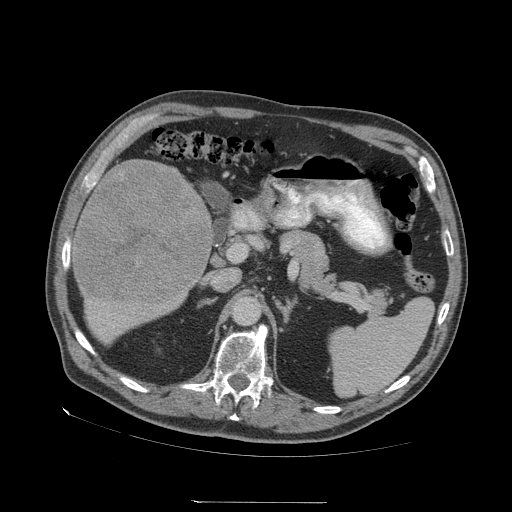
Contrast-enhanced abdominal CT (liver protocol), one axial slice. Slice 25 of 83 in the series (ordered by position). Reconstruction kernel STANDARD. 140 kVp. Soft-tissue window (W 400 / L 40 HU). 512 × 512 image matrix, field of view 460 × 460 mm. From the clinical record (not read from this slice): diagnosis: hepatocellular carcinoma (patient treated with transarterial chemoembolisation; whether this scan precedes or follows treatment is not stated here); TNM stage (as recorded): Stage-I; Child-Pugh class: A; tumour nodularity: uninodular.
Structures marked on this image (semi-automatic segmentation, software-assisted and operator-edited):
- liver parenchyma outside the tumour (the mass and vessels are separate outlines, so this box may not span the whole liver): bounding box (x1, y1, x2, y2) in pixels: (70, 159, 214, 342)
- mass: (73, 160, 209, 302)